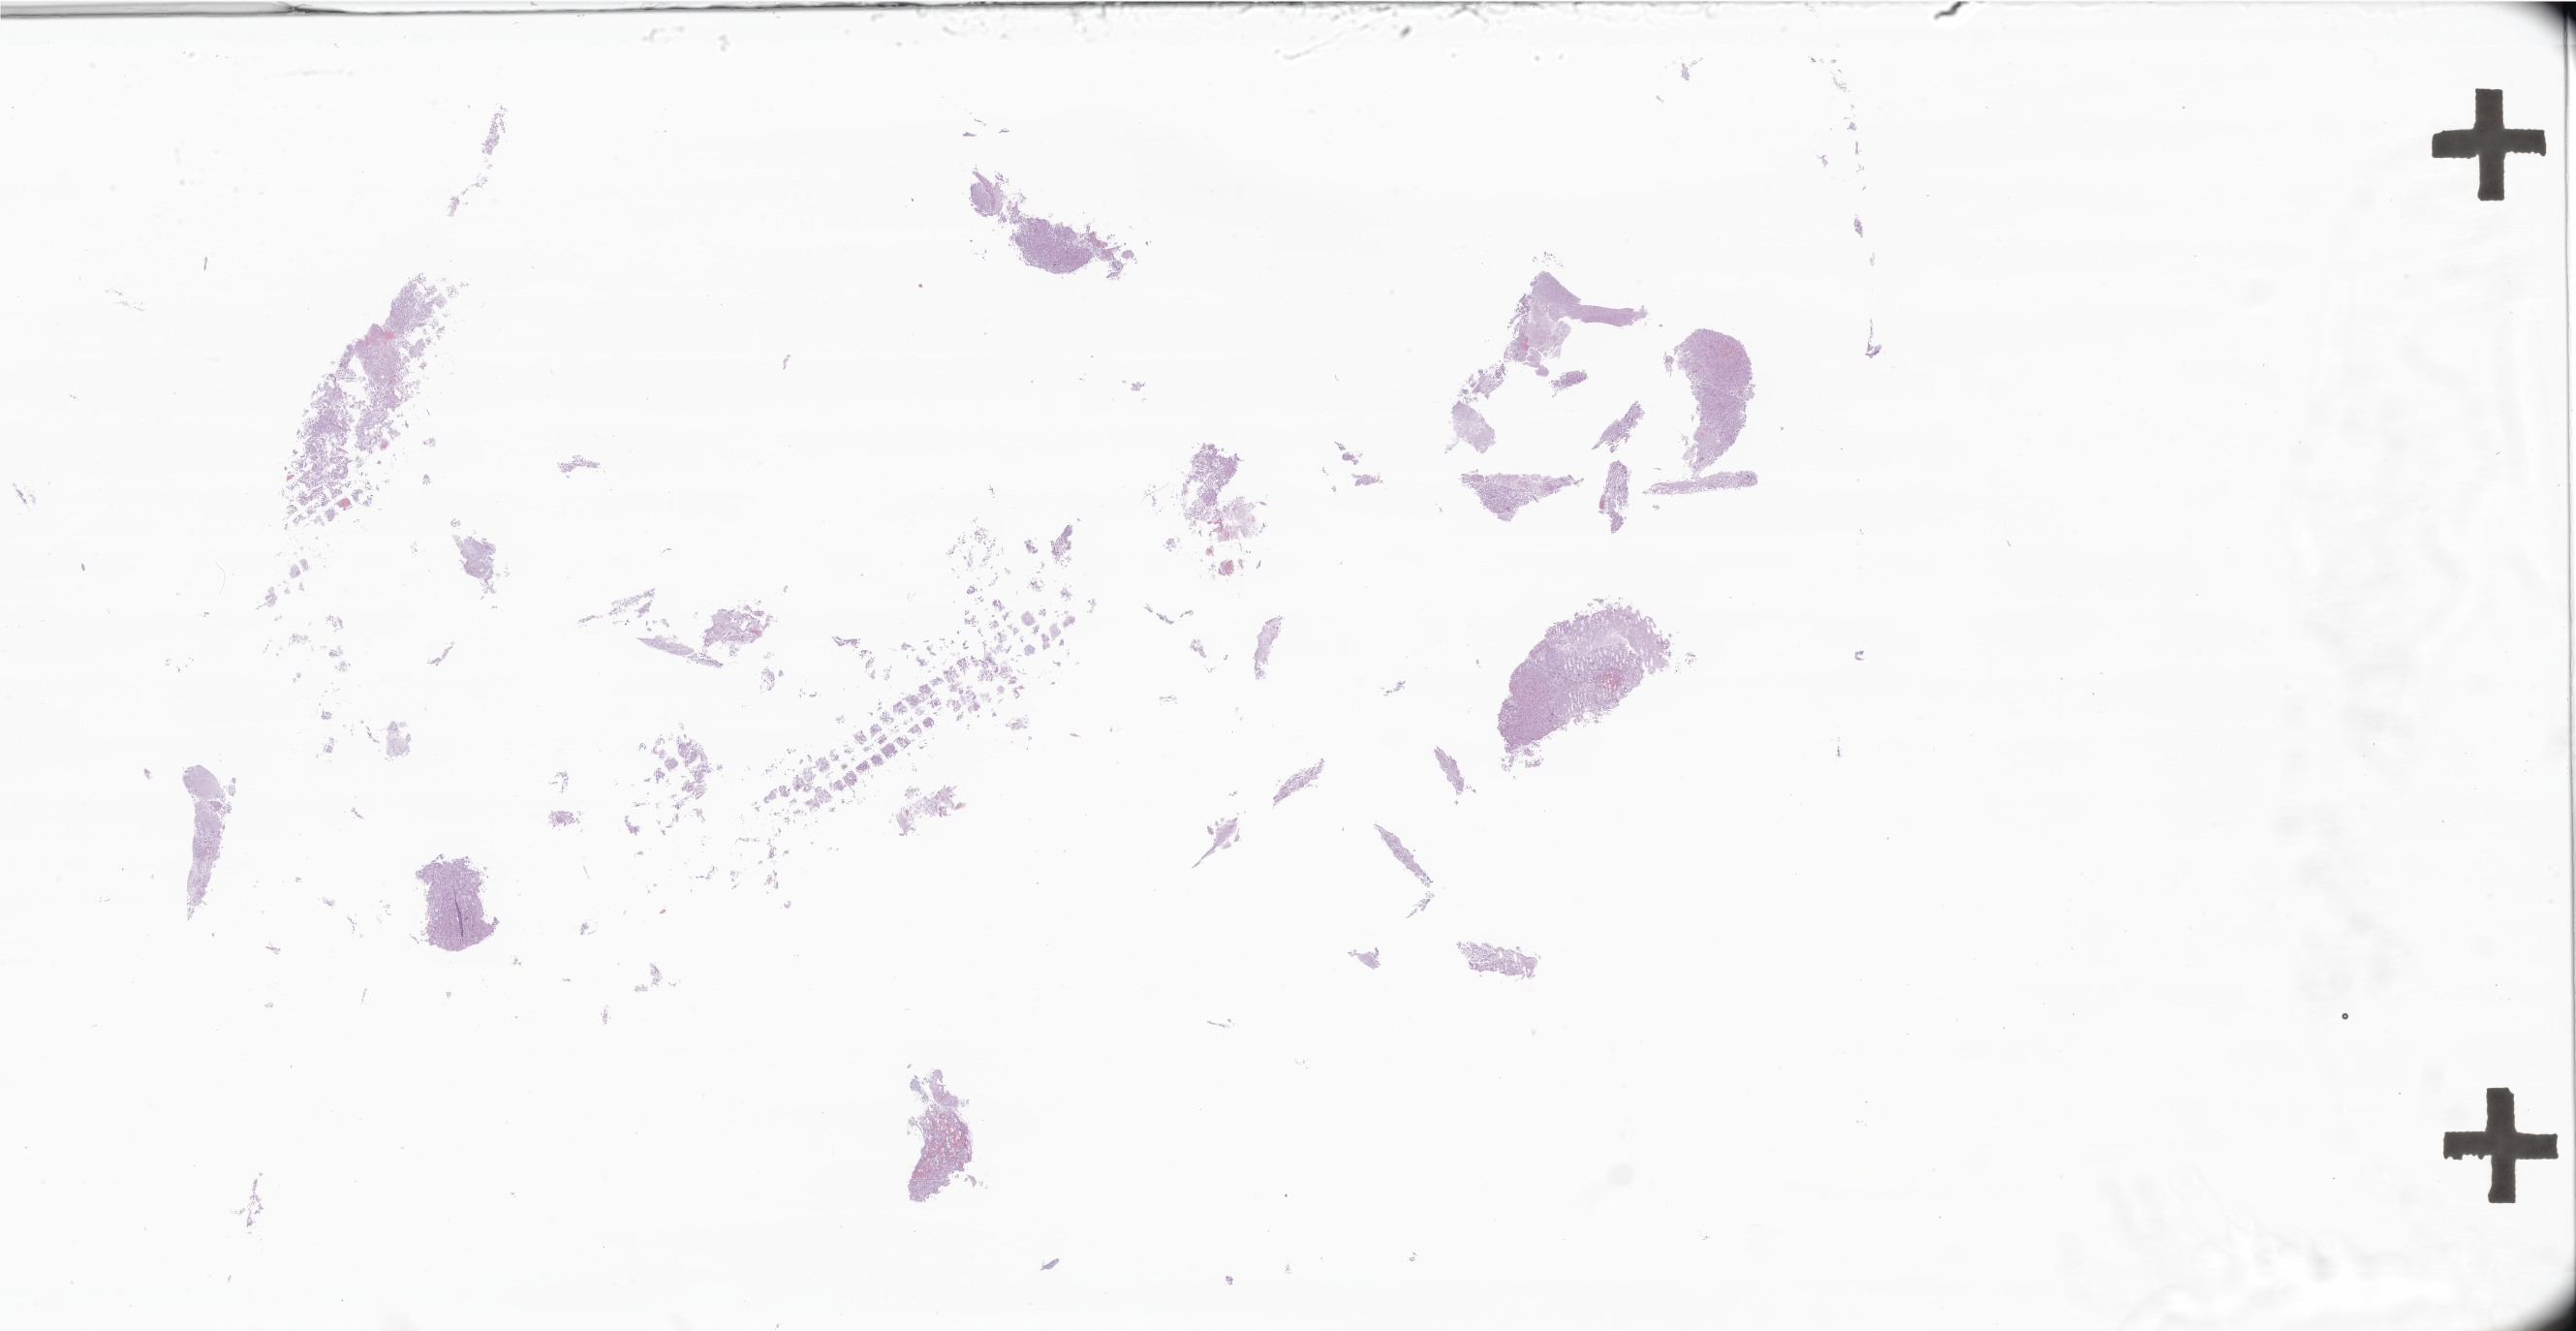
Digitized haematoxylin and eosin-stained section of tumor tissue from the brain, a low-resolution overview of the entire scanned area, about 44.8 x 23.2 mm. Formalin-fixed, paraffin-embedded (FFPE) tissue. Female patient, age 460 days.
Diagnosis (ICD-O-3 morphology term): Subependymal giant cell astrocytoma.